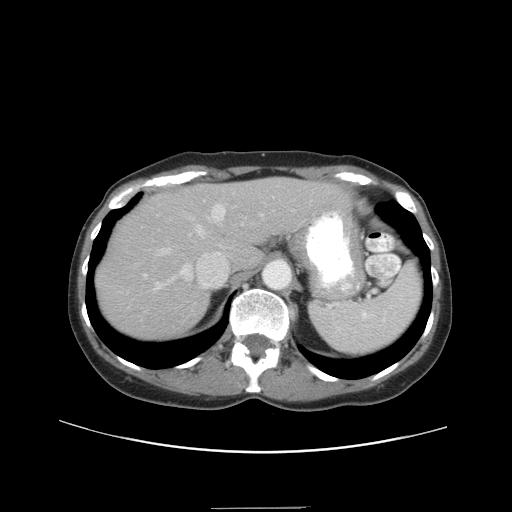
Contrast-enhanced abdominal CT, one axial slice. Position 29 of 38 along the scan axis. Reconstruction kernel STANDARD. 120 kVp. Intravenous contrast given. Soft-tissue window (W 400 / L 40 HU). 5 mm slice thickness. 512 × 512 image matrix, field of view 388 × 388 mm. Female patient, age 64 years. Case-level facts recorded for this patient, not image findings: diagnosis: colorectal cancer liver metastases, imaged before liver resection; multiple liver metastases: no; largest metastasis: 3.8 cm; chemotherapy before resection: yes.
Outlined on this slice (expert manual segmentation):
- hepatic veins: bounding box (x1, y1, x2, y2) in pixels: (152, 205, 243, 291)
- liver: (99, 180, 342, 338)
- planned liver remnant (the part of the liver to remain after resection): (145, 180, 342, 266)
- portal vein (with intrahepatic branches): (144, 214, 263, 277)